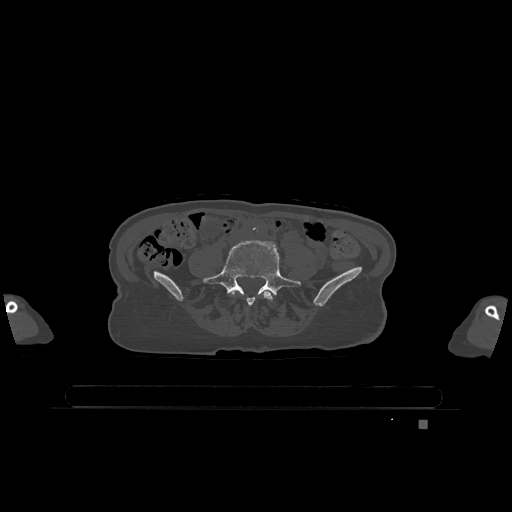
CT including the spine, one axial slice. Slice 252 of 1317 in the series (ordered by position). Bone window (W 1800 / L 400 HU). 512 × 512 image matrix, field of view 500 × 500 mm. Female patient, age 74 years. Case-level facts recorded for this patient, not image findings: primary cancer: lung.
Structures marked on this image (semi-automatic segmentation, software-assisted and operator-edited):
- L4 vertebra: bounding box (x1, y1, x2, y2) in pixels: (231, 291, 273, 302)
- L5 vertebra: (204, 240, 301, 305)